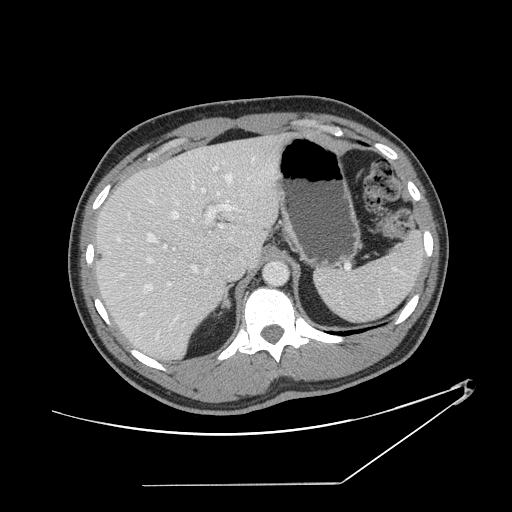
Contrast-enhanced abdominal CT, one axial slice. Position 101 of 152 along the scan axis. Reconstruction kernel STANDARD. 120 kVp. Intravenous contrast given. Soft-tissue window (W 400 / L 40 HU). 2.5 mm slice thickness. 512 × 512 image matrix, field of view 432 × 432 mm. Male patient, age 45 years. Case-level facts recorded for this patient, not image findings: diagnosis: colorectal cancer liver metastases, imaged before liver resection; multiple liver metastases: no; largest metastasis: 1 cm; disease in both lobes: no.
Annotated regions visible in this slice (outlined manually by an expert reader):
- hepatic veins: bounding box [x1, y1, x2, y2] px = [115, 157, 255, 321]
- liver: [98, 136, 285, 358]
- planned liver remnant (the part of the liver to remain after resection): [98, 154, 232, 358]
- portal vein (with intrahepatic branches): [139, 167, 236, 340]